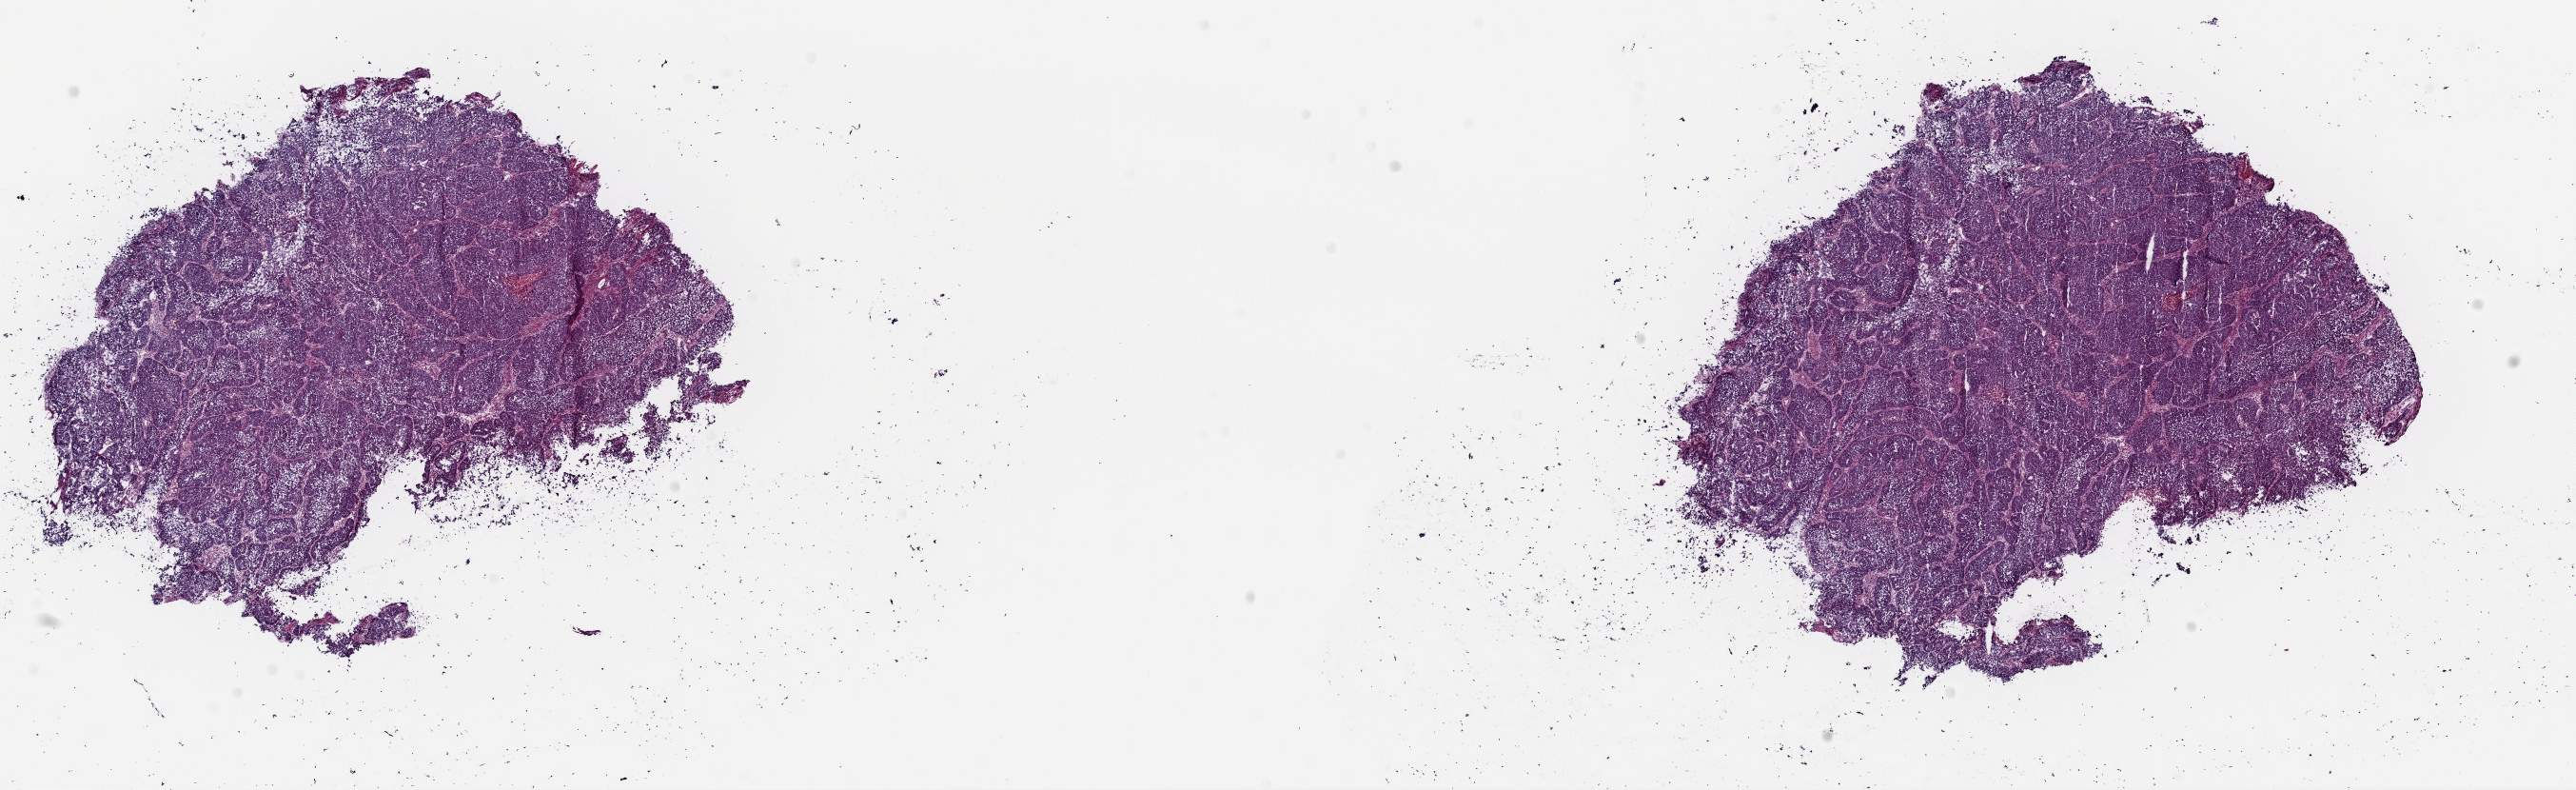
Digitized H&E tissue section (whole slide) — whole scanned area (about 21.4 x 6.6 mm, acquisition: 40x scan) shown as a low-resolution overview. Frozen section from the top of the tissue portion. Sample: primary tumour, uterus. Patient: female, age at initial diagnosis 71 years.
Histologic diagnosis: Endometrioid adenocarcinoma, NOS (endometrium).